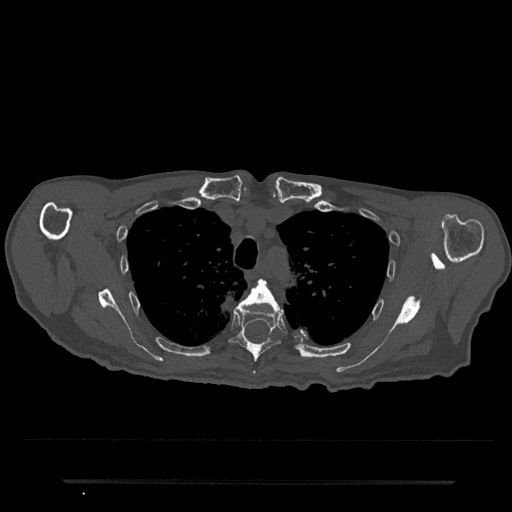
CT including the spine, one axial slice; reconstruction kernel Br40s/3; 120 kVp; bone window (W 1800 / L 400 HU); 512 × 512 image matrix. Male patient, age 74 years. From the clinical record (not read from this slice): primary cancer: prostate.
Annotated regions visible in this slice (semi-automatically segmented with operator editing):
- T4 vertebra: bounding box <244,279,283,315> (left, top, right, bottom; pixels)
- T5 vertebra: <231,299,282,362>